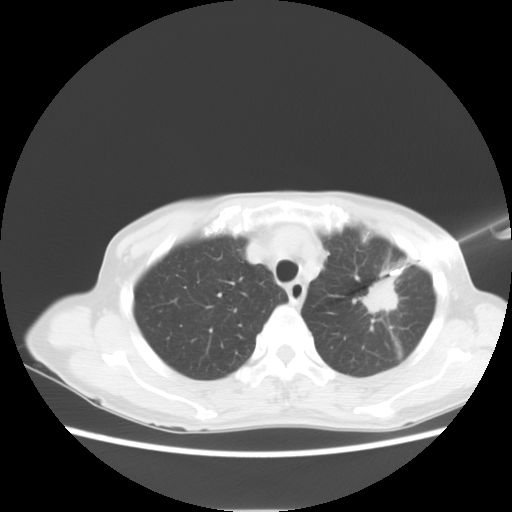
Chest CT, one axial slice; reconstruction kernel STANDARD; 120 kVp; lung window (W 1500 / L -600 HU); 5 mm slice thickness; 512 × 512 image matrix, field of view 350 × 350 mm. Patient: female, 71 years. From the clinical record (not read from this slice): clinical TNM (as recorded): T2 N0 M0.
Outlined on this slice (rectangle marked by the reading radiologist):
- lung tumour (recorded histology: adenocarcinoma): bounding box (x1, y1, x2, y2) in pixels: (363, 273, 403, 320)